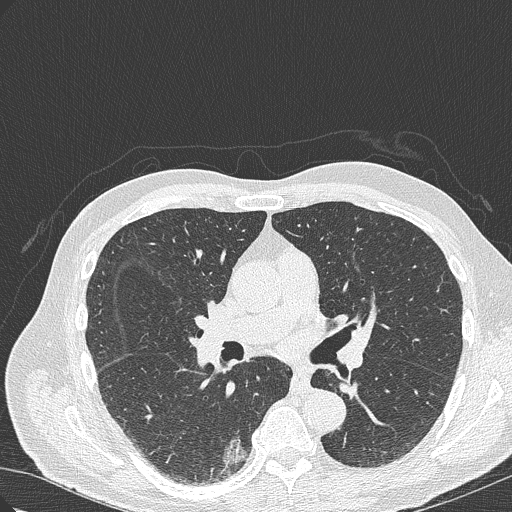
Low-dose screening chest CT, axial slice, first (baseline) screen, lung window (W 1500 / L -600 HU), 1 mm slice thickness, slice 140 of 322 in the series, 512 × 512 image matrix, field of view 350 × 350 mm. Male, age 70 years at enrolment. Current smoker at enrolment.
- Lesion marked by an expert reader, bounding box (x1, y1, x2, y2) in pixels: (198, 419, 261, 477).
- The screening reader recorded 4 non-calcified nodules or masses ≥4 mm on this exam (right lower lobe, right lower lobe, right upper lobe, right lower lobe); which of them this box marks is not recorded.